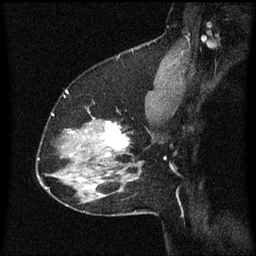
Breast MRI (dynamic contrast-enhanced), one sagittal slice; position 45 of 60 along the scan axis; dynamic contrast-enhanced series, image 2 of 3 at this slice position (ordered by acquisition); 1.5 T; TE 4.2 ms, TR 8.4 ms; 2 mm slice thickness; 256 × 256 image matrix, field of view 200 × 200 mm. Patient: female, 37 years. Case-level facts recorded for this patient, not image findings: setting: breast cancer imaged before/during neoadjuvant chemotherapy; receptor status: HR-positive, HER2-negative.
Outlined on this slice (semi-automatically segmented with operator editing):
- analysis volume of interest (the breast-tissue region the enhancement analysis was run in; not a lesion): bounding box [x1, y1, x2, y2] px = [94, 118, 130, 157]
- tumour enhancement mask (voxels above the 70 % enhancement threshold inside the analysis volume of interest): [105, 122, 128, 157]